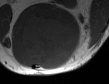
MRI of an extremity soft-tissue mass, one axial slice; position 33 of 50 along the scan axis; MR volume resampled by the dataset authors to the PET/CT grid (not the native acquisition matrix); 109 × 84 image matrix. Male patient. From the clinical record (not read from this slice): histological type: synovial sarcoma; site of the primary tumour: left poplietal fossa.
Structures marked on this image (expert contour drawn on MRI and transferred to this co-registered scan by the dataset authors):
- gross tumour volume (mass): bounding box [x1, y1, x2, y2] px = [18, 16, 76, 68]